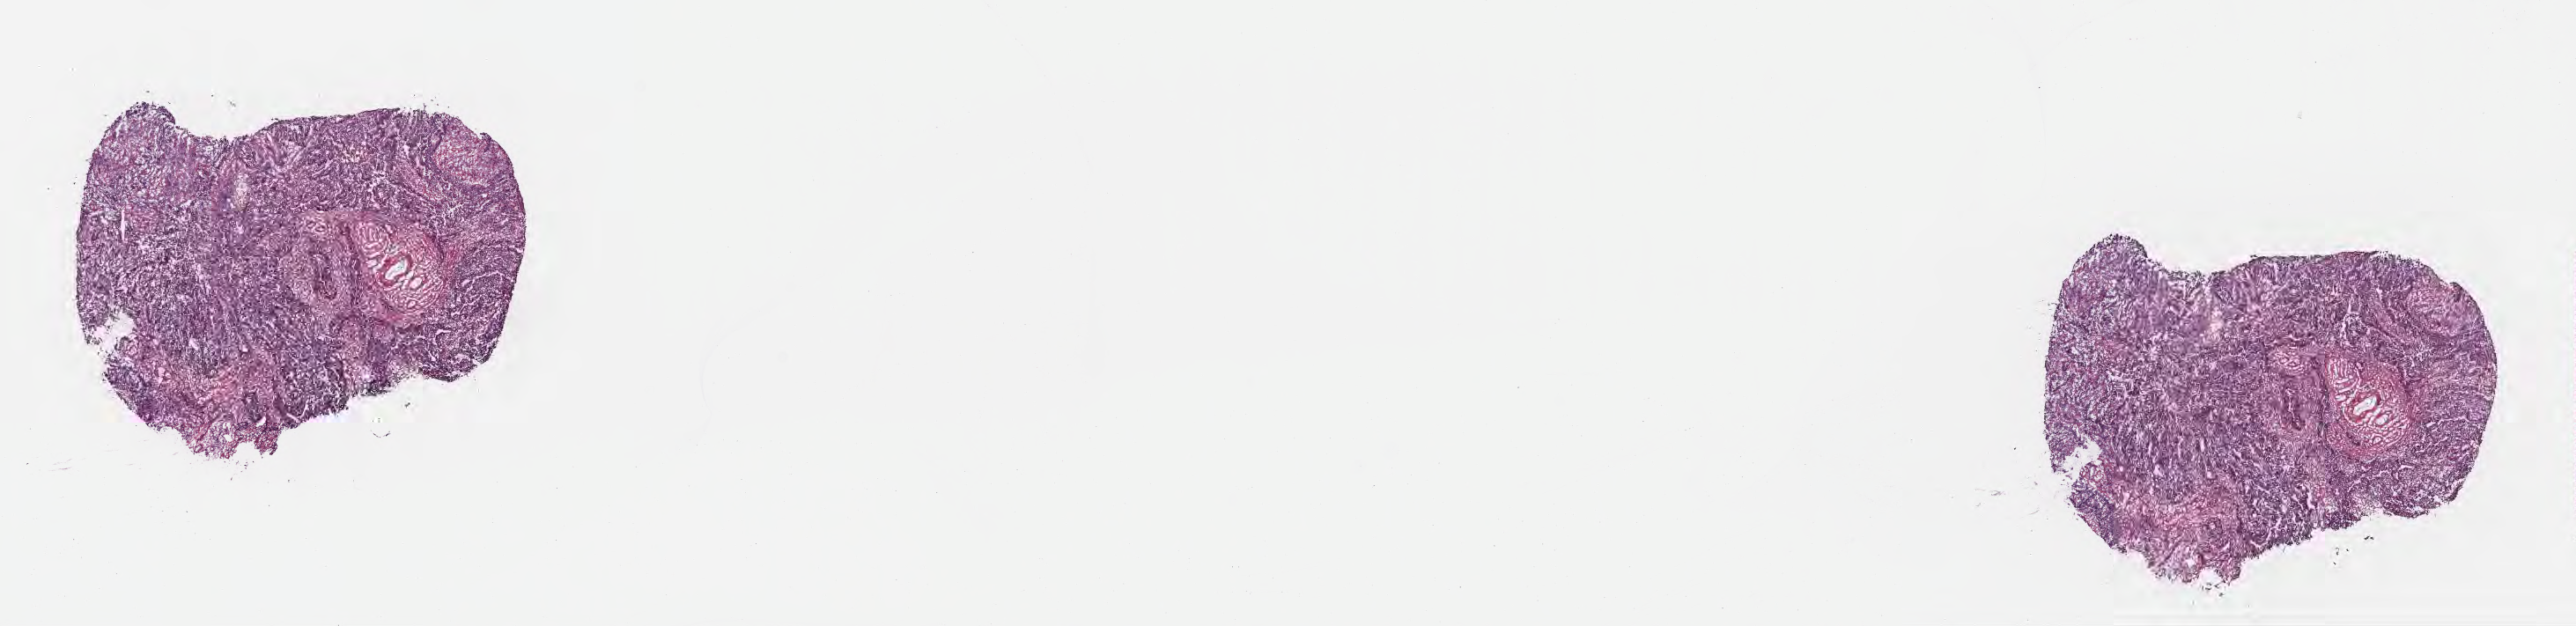
Digitized H&E-stained section — shown as a low-resolution overview of the whole scanned area (about 23.6 x 5.7 mm), frozen section, specimen: primary tumor, site: sigmoid colon. Female patient; age at initial diagnosis 55 years. Pathologist review of this section (percent, as recorded): tumor cells 80%, tumor nuclei 80%, stromal cells 17%, necrosis 1%, normal cells 2%. Infiltration values recorded for this section: lymphocyte infiltration 3%, monocyte infiltration 2%, neutrophil infiltration 6%.
Section: top of the tissue portion. Diagnosis: Adenocarcinoma, NOS.